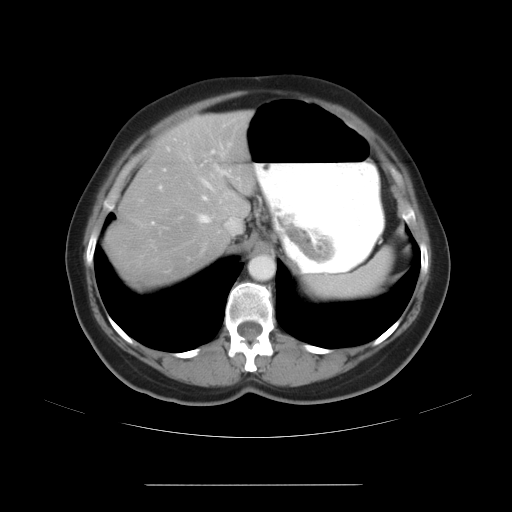
Contrast-enhanced abdominal CT, one axial slice; position 21 of 27 along the scan axis; reconstruction kernel STANDARD; intravenous contrast given; soft-tissue window (W 400 / L 40 HU); 7.5 mm slice thickness; 512 × 512 image matrix. Female patient, age 58 years. From the clinical record (not read from this slice): diagnosis: colorectal cancer liver metastases, imaged before liver resection; multiple liver metastases: yes; largest metastasis: 1.9 cm.
Structures marked on this image (expert manual segmentation):
- hepatic veins: bounding box <197,167,238,240> (left, top, right, bottom; pixels)
- liver: <109,114,254,283>
- planned liver remnant (the part of the liver to remain after resection): <124,115,253,226>
- portal vein (with intrahepatic branches): <152,124,225,224>
- liver metastasis: <141,240,160,251>